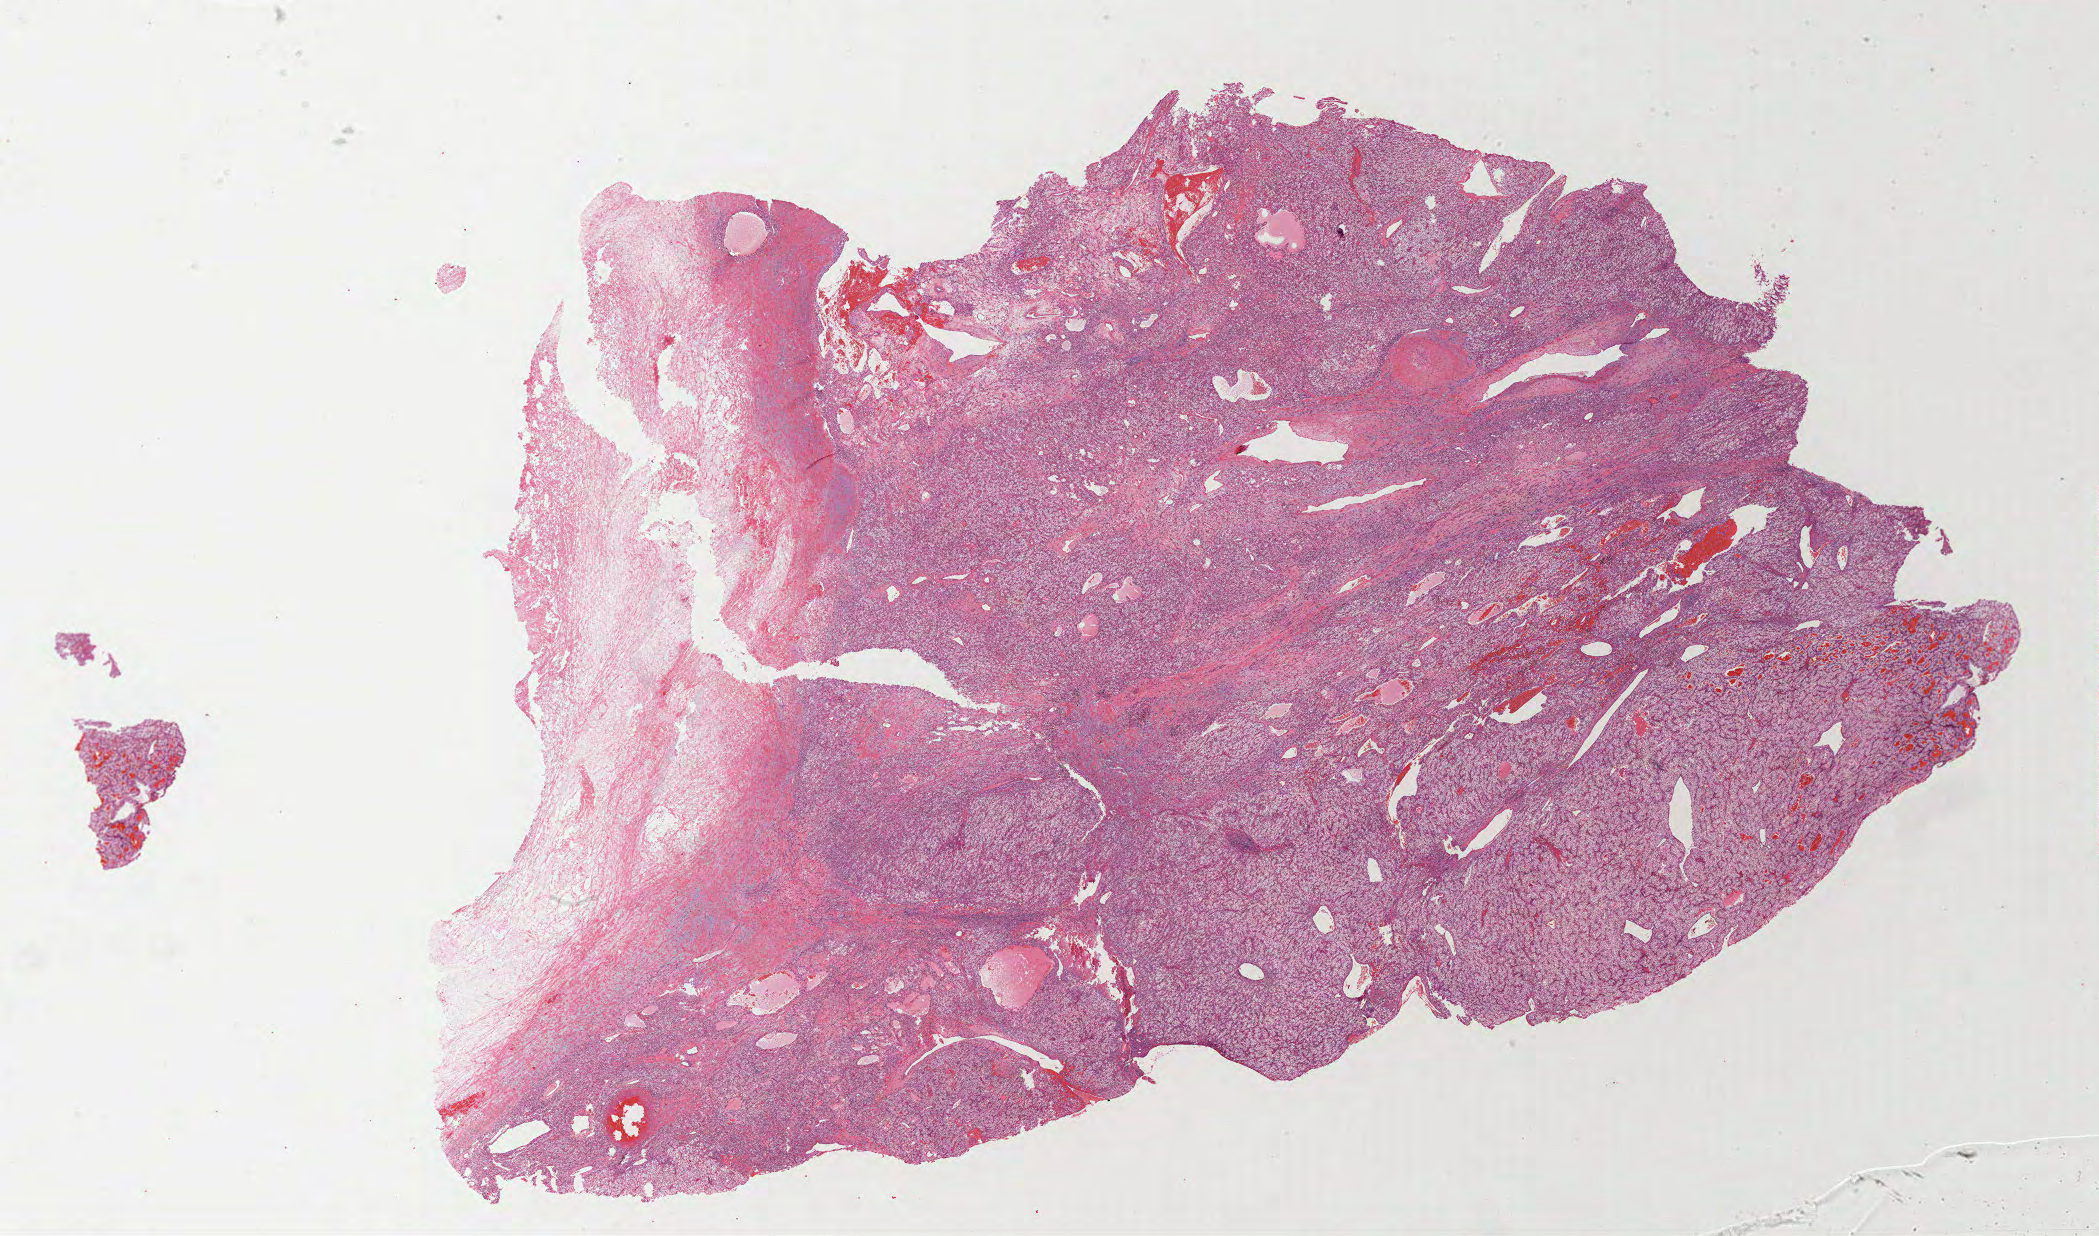
Whole-slide histology image, H&E, shown as a low-resolution overview of the whole scanned area (about 33.8 x 19.9 mm, from a 40x scan); formalin-fixed paraffin-embedded (FFPE) diagnostic section; sample: primary tumour, kidney. Male patient; age at initial diagnosis 57 years. Histologic grade: G3 (poorly differentiated).
Laterality: left. Lymph nodes positive (case pathology): 0 of 7 examined. AJCC pathologic stage: II. Pathologic diagnosis: Clear cell adenocarcinoma, NOS.